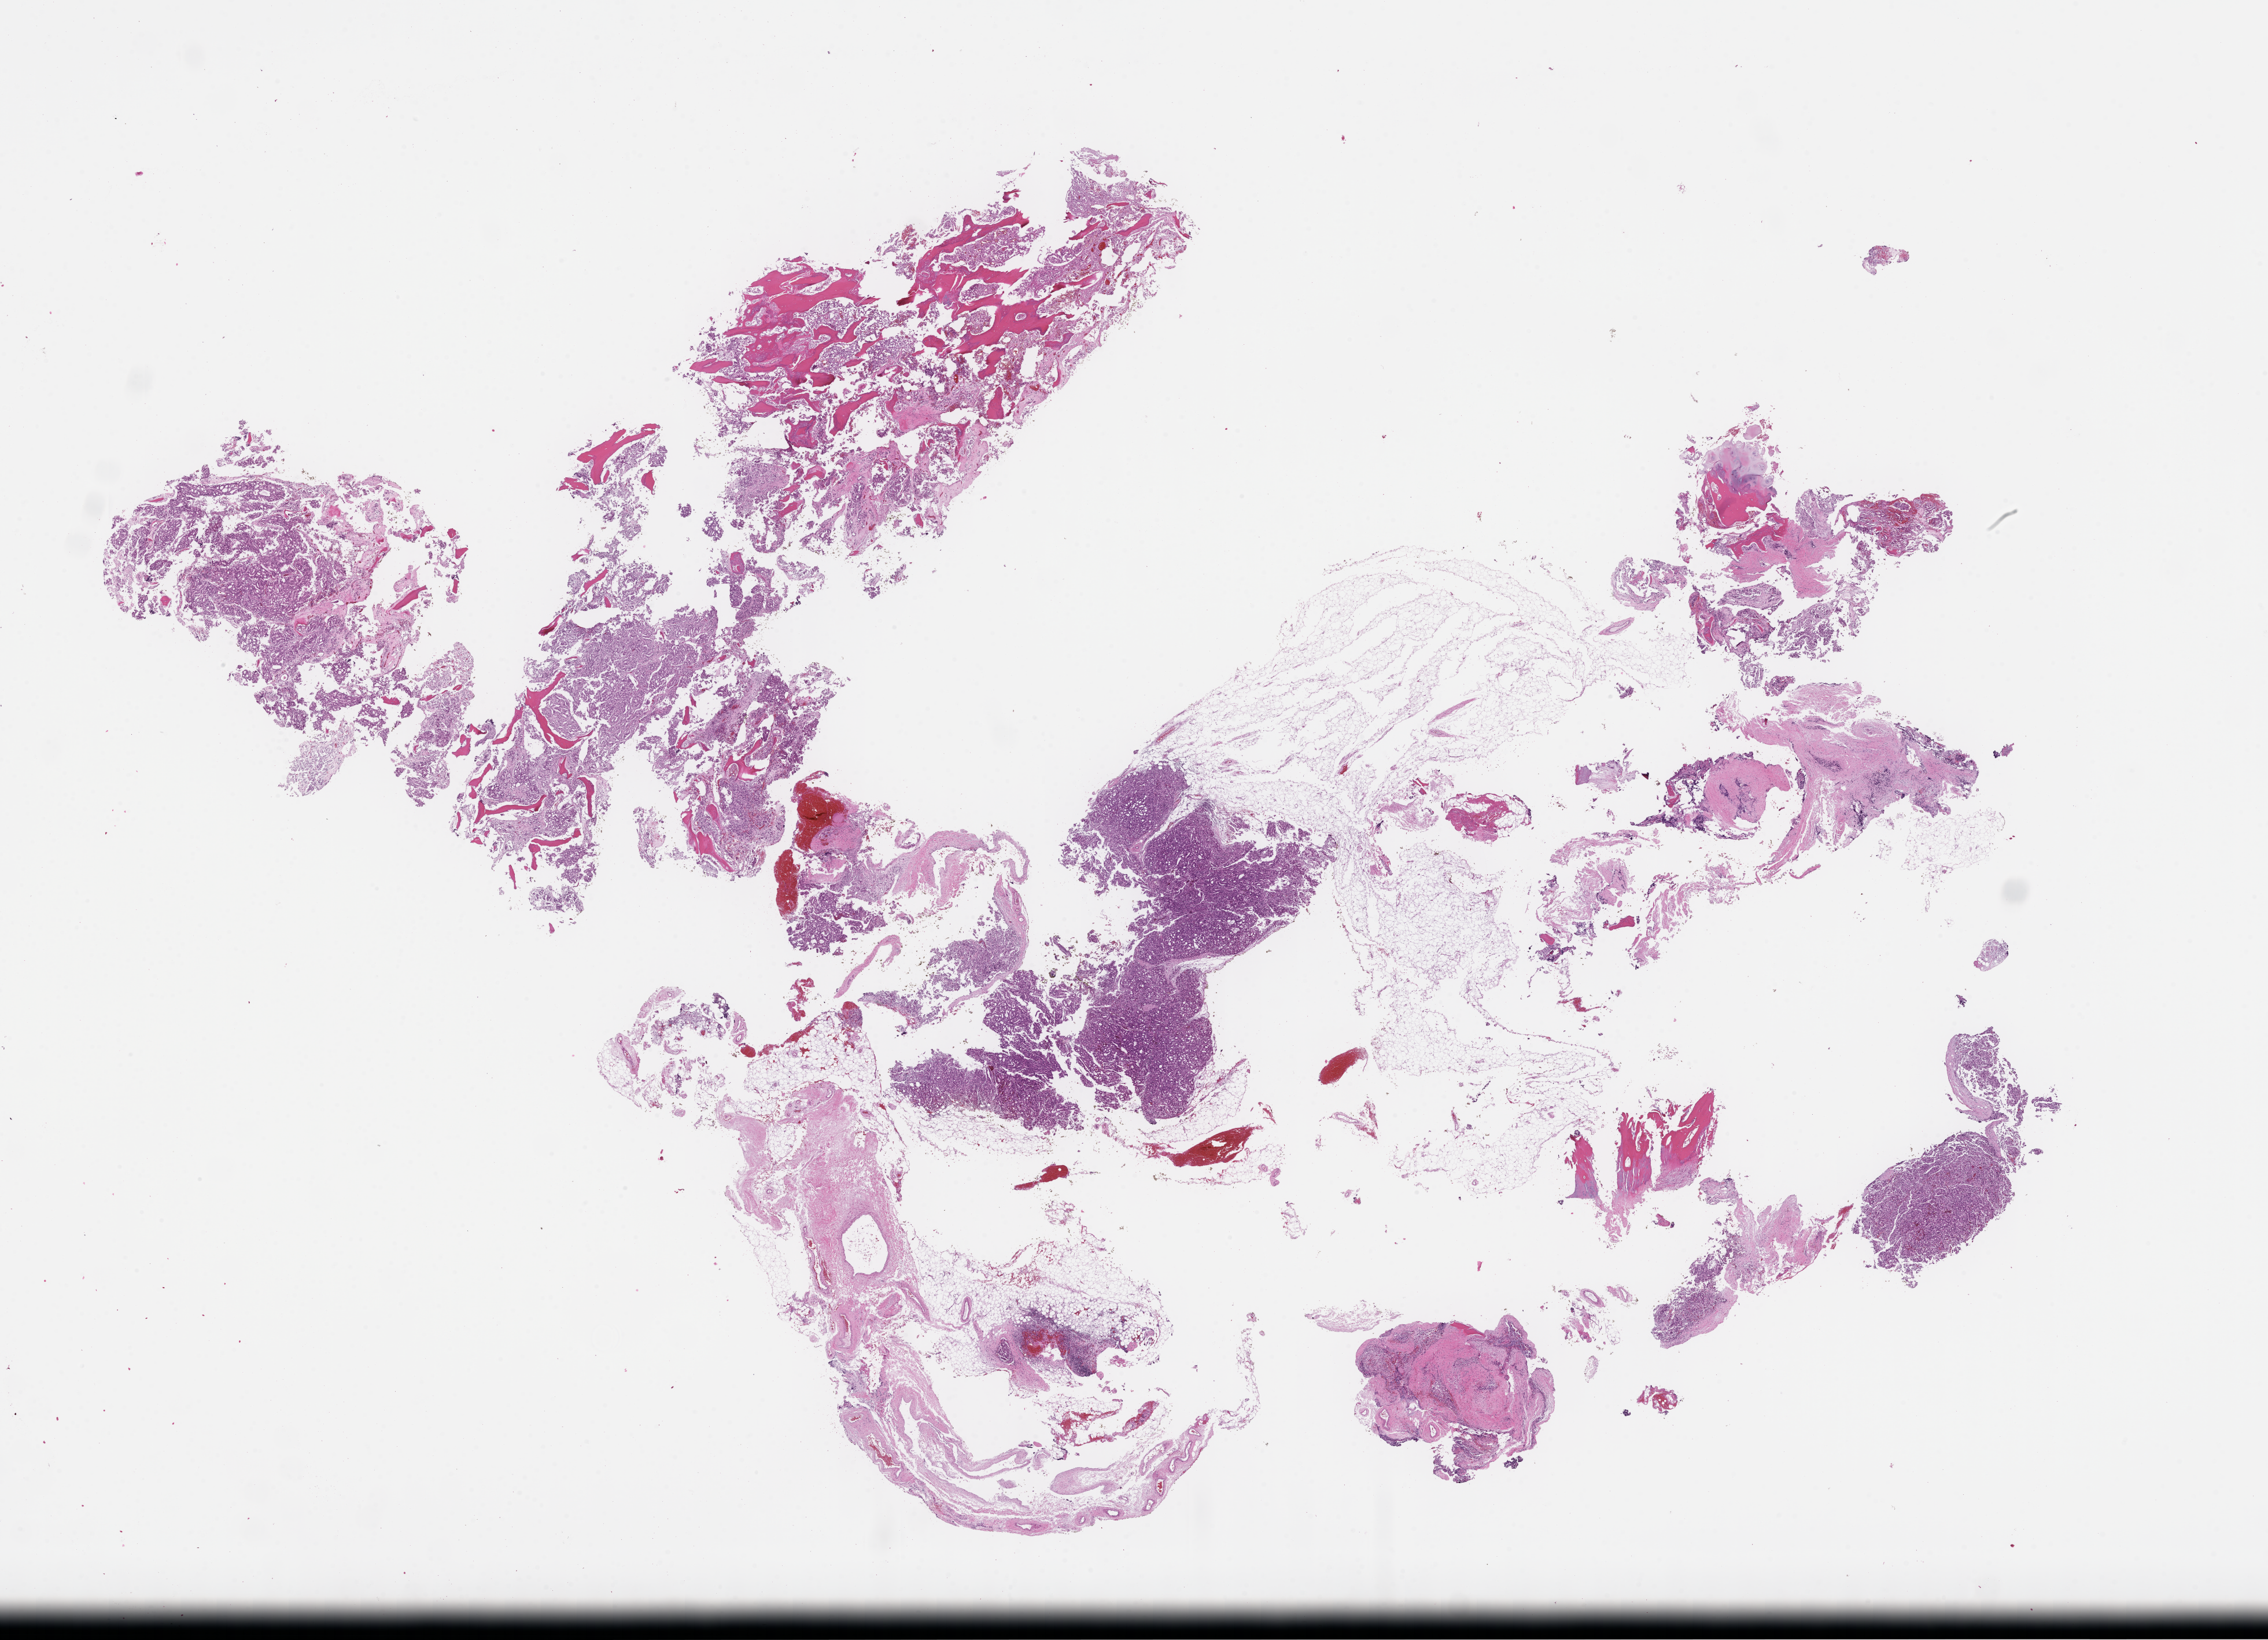
Digitized haematoxylin and eosin-stained section — whole scanned area (about 31.7 x 22.9 mm) shown as a low-resolution overview. Formalin-fixed, paraffin-embedded (FFPE) tissue. Patient: male.
This section: metastatic tumor tissue. Patient diagnosis (primary): Prostate Carcinoma.